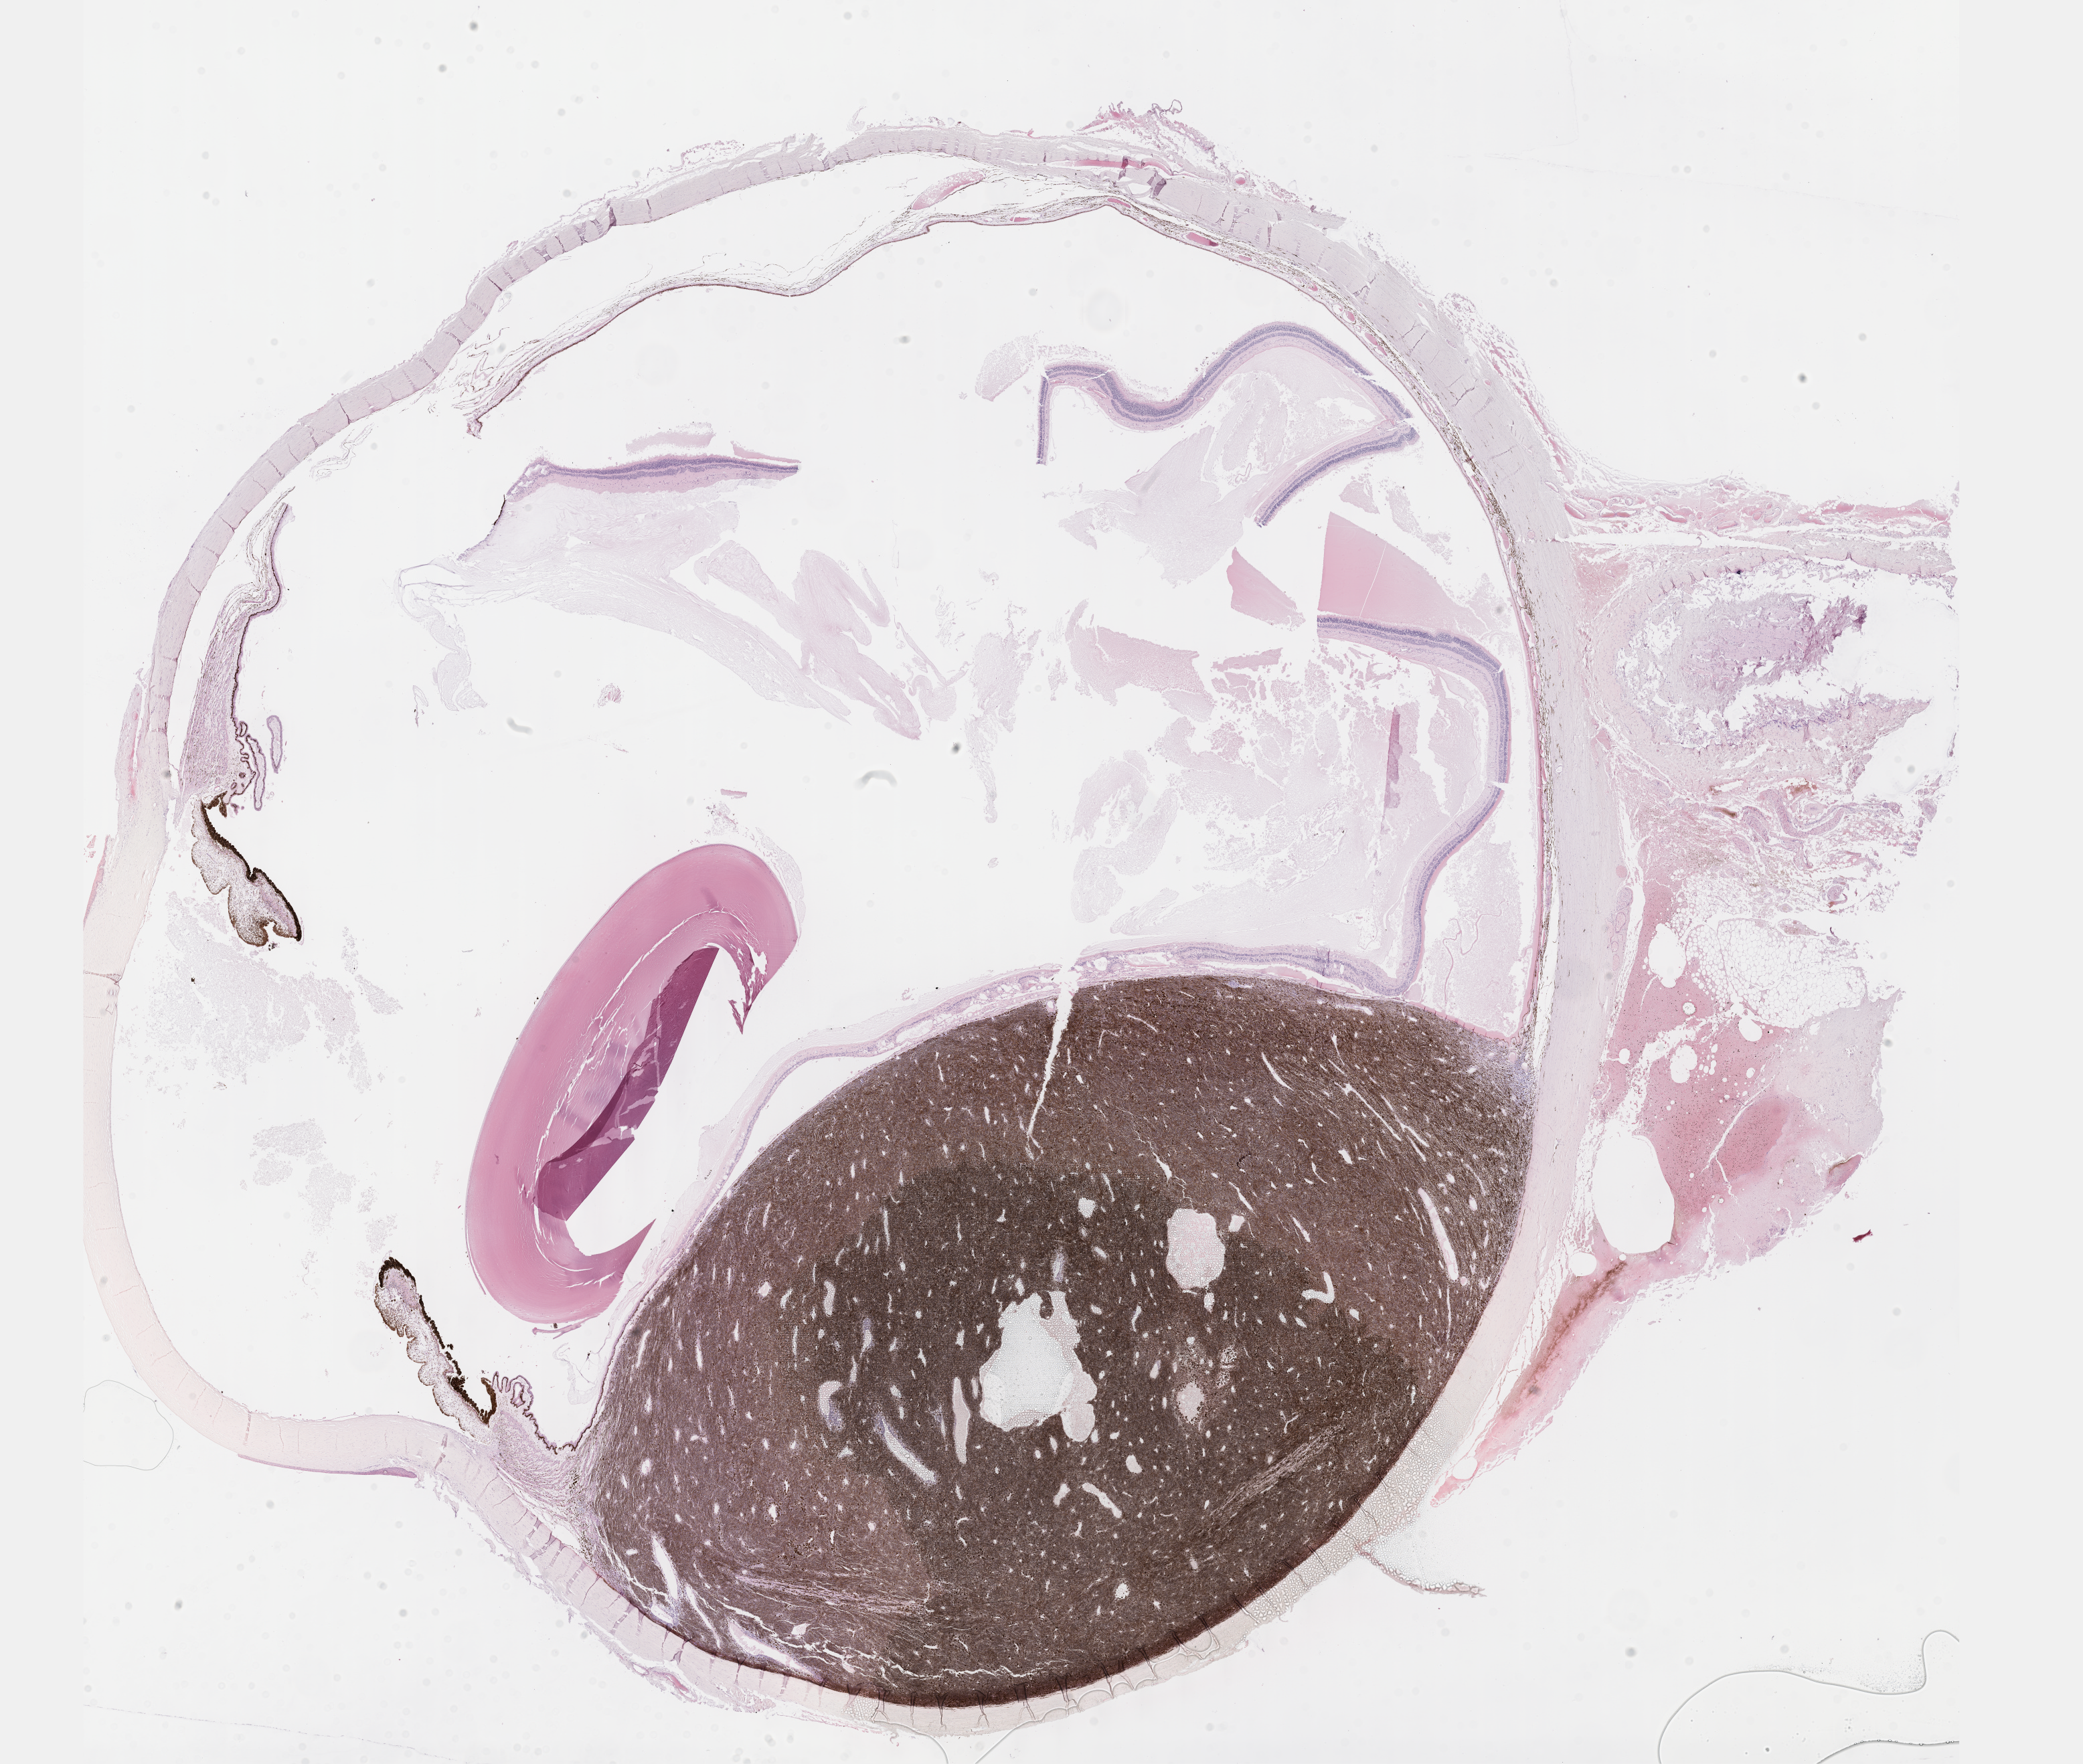
Digitized H&E tissue section (whole slide), a low-resolution overview of the entire scanned area, about 25.1 x 21.3 mm (acquisition: 40x scan); formalin-fixed paraffin-embedded (FFPE) diagnostic section; uvea, primary tumour sample. Female patient; age at initial diagnosis 37 years.
Histologic diagnosis: Spindle cell melanoma, NOS. AJCC pathologic stage: IIB (7th edition).